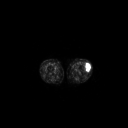
FDG PET of an extremity soft-tissue mass (from a PET/CT study), one axial slice. Slice 175 of 223 in the series (ordered by position). 3.27 mm slice thickness. 128 × 128 image matrix, field of view 700 × 700 mm. Patient: female, 16 years. Case-level facts recorded for this patient, not image findings: histological type: spindle cell suggestive of biphasic synovial sarcoma; grade: intermediate; site of the primary tumour: left knee.
Structures marked on this image (expert contour drawn on MRI and transferred to this co-registered scan by the dataset authors):
- gross tumour volume including surrounding oedema: bounding box <85,61,91,71> (left, top, right, bottom; pixels)
- gross tumour volume (mass): <85,62,91,71>